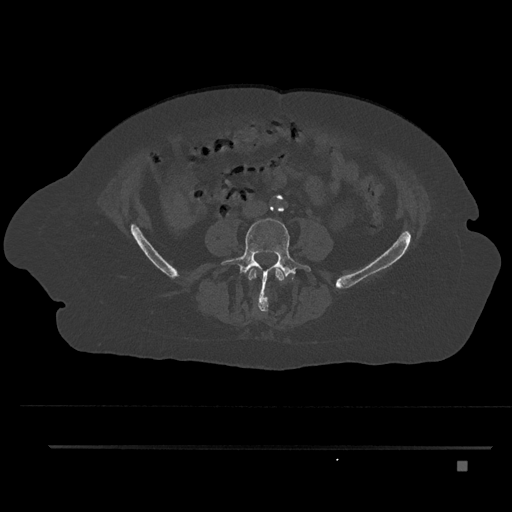
CT including the spine, one axial slice. Slice 89 of 797 in the series (ordered by position). Reconstruction kernel Br40s/3. Bone window (W 1800 / L 400 HU). 0.5 mm slice thickness. 512 × 512 image matrix, field of view 437 × 437 mm. Female patient, age 76 years. From the clinical record (not read from this slice): primary cancer: lung; vertebrae with lytic lesions (as recorded): T11, L3.
Outlined on this slice (semi-automatic segmentation, software-assisted and operator-edited):
- L3 vertebra: bounding box [x1, y1, x2, y2] px = [248, 267, 285, 312]
- L4 vertebra: [220, 218, 311, 311]